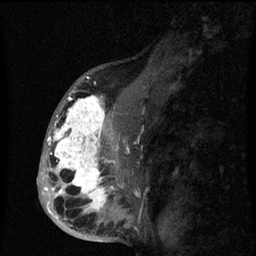
Breast MRI (dynamic contrast-enhanced), one sagittal slice. Slice 37 of 60 in the series (ordered by position). Dynamic contrast-enhanced series, image 2 of 3 at this slice position (ordered by acquisition). 1.5 T. TE 4.2 ms, TR 8 ms. 256 × 256 image matrix, field of view 190 × 190 mm. Female patient, age 50 years.
Structures marked on this image (semi-automatic segmentation, software-assisted and operator-edited):
- analysis volume of interest (the breast-tissue region the enhancement analysis was run in; not a lesion): bounding box [x1, y1, x2, y2] px = [43, 90, 141, 216]
- tumour enhancement mask (voxels above the 70 % enhancement threshold inside the analysis volume of interest): [44, 91, 122, 216]